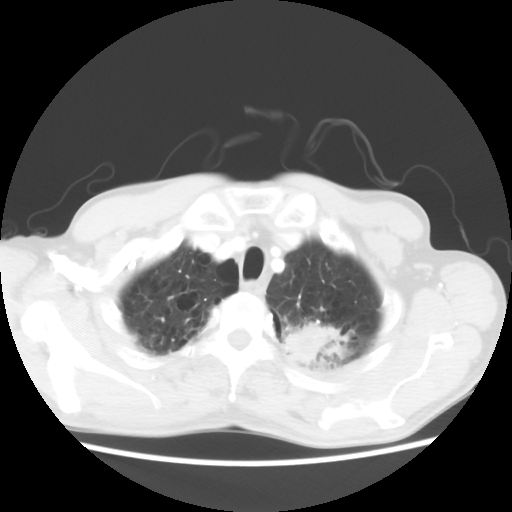
Chest CT, one axial slice. Slice 56 of 64 in the series (ordered by position). Reconstruction kernel STANDARD. 120 kVp. Lung window (W 1500 / L -600 HU). 512 × 512 image matrix, field of view 346 × 346 mm. Male patient, age 63 years. Case-level facts recorded for this patient, not image findings: clinical TNM (as recorded): T2 N0 M0.
Outlined on this slice (bounding box drawn by a radiologist):
- lung tumour (recorded histology: adenocarcinoma): bounding box <284,314,345,375> (left, top, right, bottom; pixels)